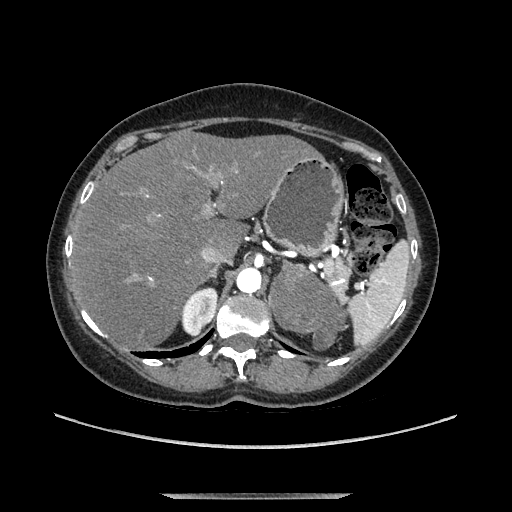
Contrast-enhanced abdominal CT, one axial slice. Soft-tissue window (W 400 / L 40 HU). 1.25 mm slice thickness. 512 × 512 image matrix, field of view 400 × 400 mm. Female patient. Case-level facts recorded for this patient, not image findings: diagnosis: adrenocortical carcinoma; tumour side: left adrenal; tumour size at pathology: 9 cm; Ki-67 index: 2 %; stage (as recorded): 3.
Annotated regions visible in this slice (semi-automatic segmentation, software-assisted and operator-edited):
- mass: bounding box <272,262,343,346> (left, top, right, bottom; pixels)